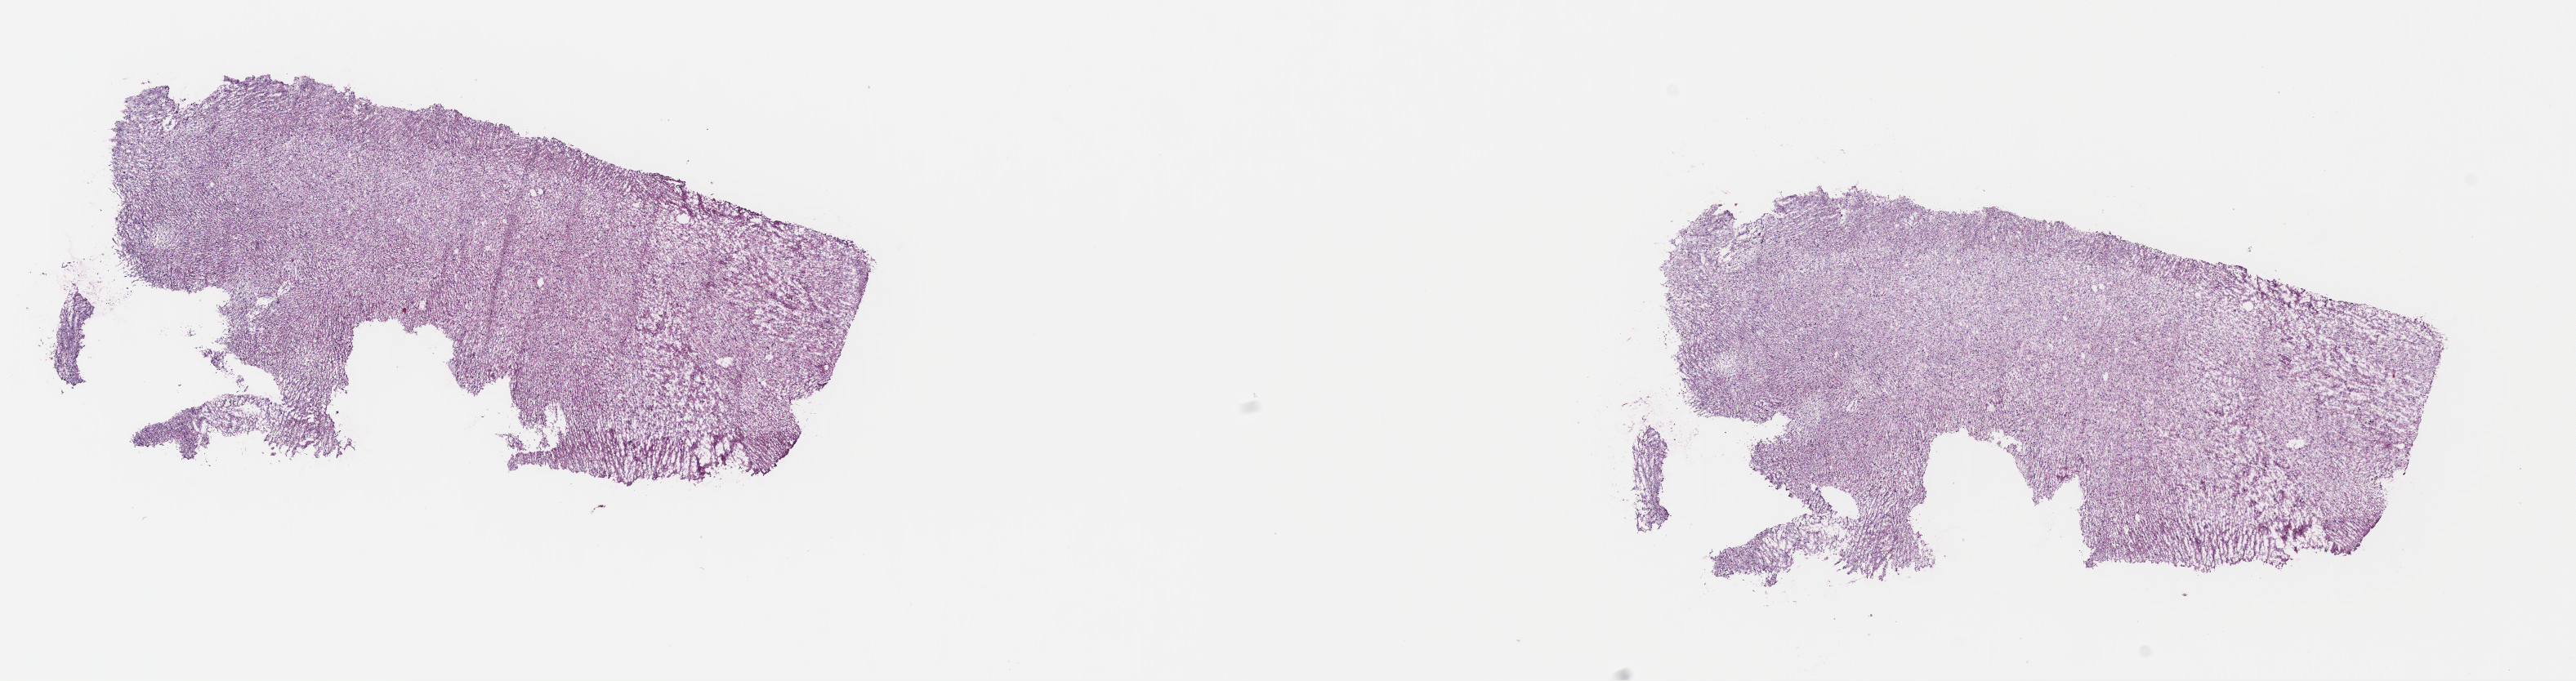
Whole-slide histology image, Hematoxylin and eosin (H&E) stained — whole scanned area (about 24.8 x 6.6 mm) shown as a low-resolution overview, frozen section from the top of the tissue portion, sample: primary tumour, brain. Patient: female, age at initial diagnosis 22 years.
Histologic diagnosis: Astrocytoma, anaplastic (cerebrum).